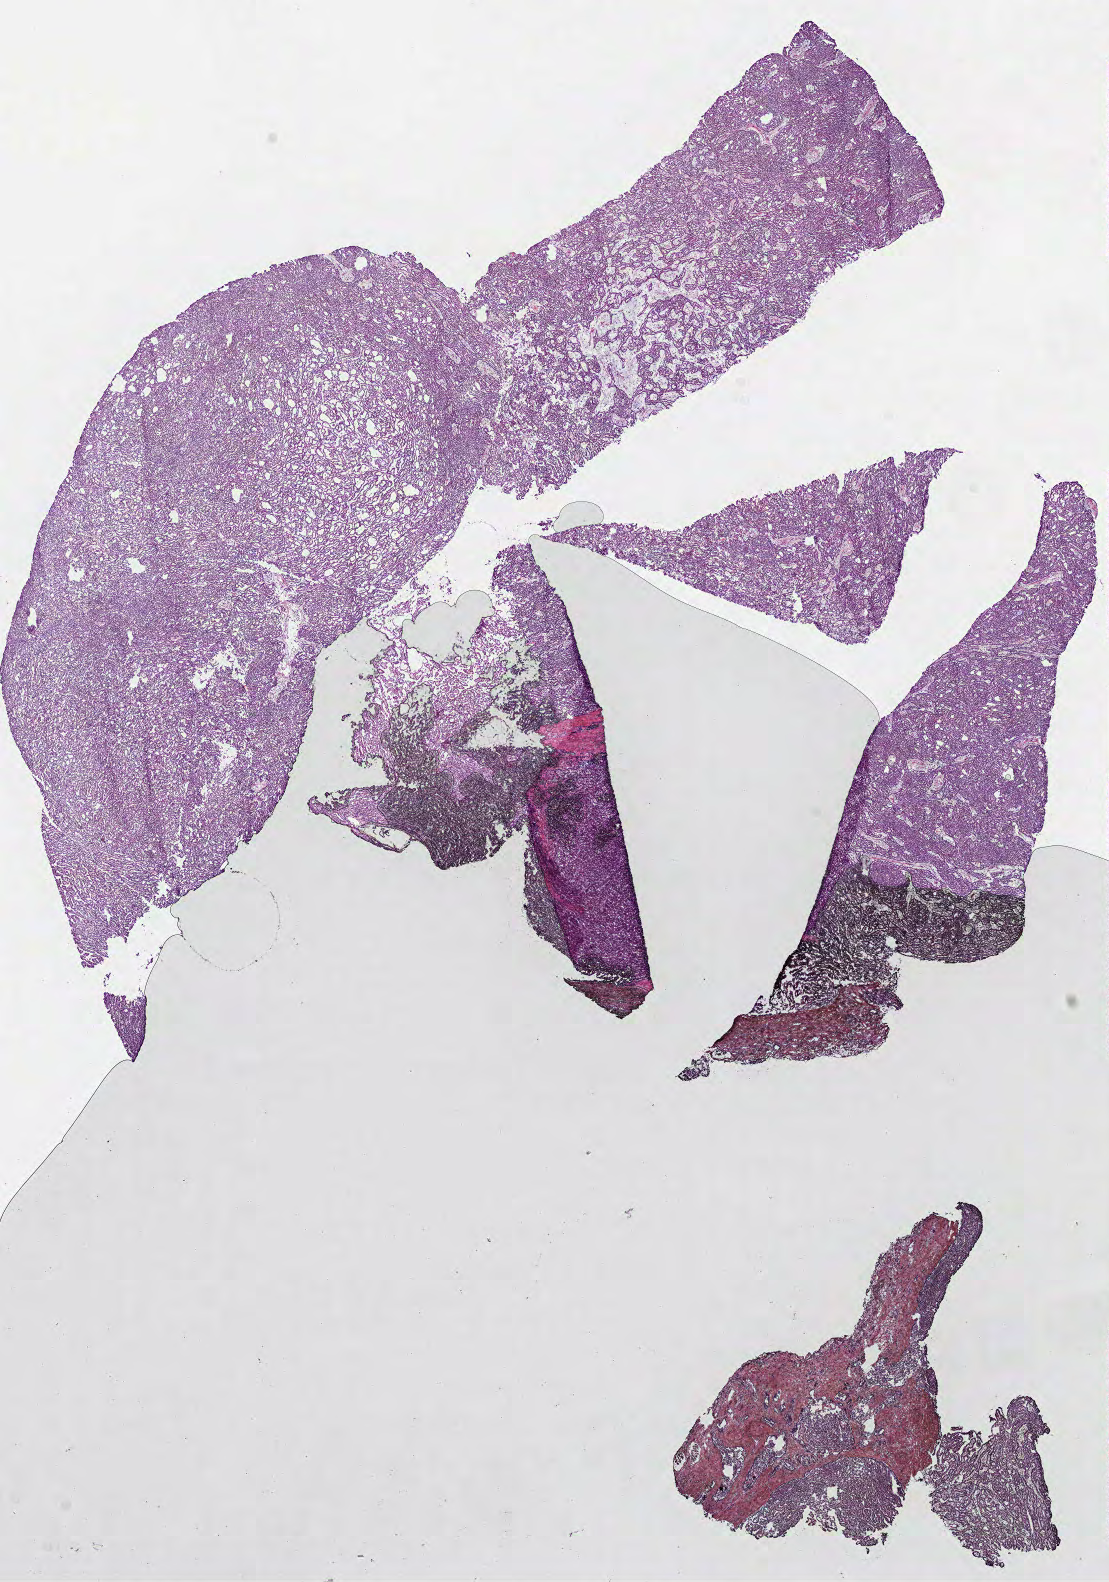
Whole-slide histology image, Hematoxylin and eosin (H&E) stained — shown as a low-resolution overview of the whole scanned area (about 8.9 x 12.8 mm, from a 40x scan). Frozen section from the bottom of the tissue portion. Primary tumour sample from the kidney. Male, age 52 years at initial diagnosis. Pathologist review of this section (percent, as recorded): tumour cells 98%, tumour nuclei 95%, normal cells 0%, stromal cells 2%, necrosis 0%.
* TNM: T1a NX MX
* pathologic diagnosis: Papillary adenocarcinoma, NOS
* AJCC pathologic stage: I (7th edition)
* laterality: left